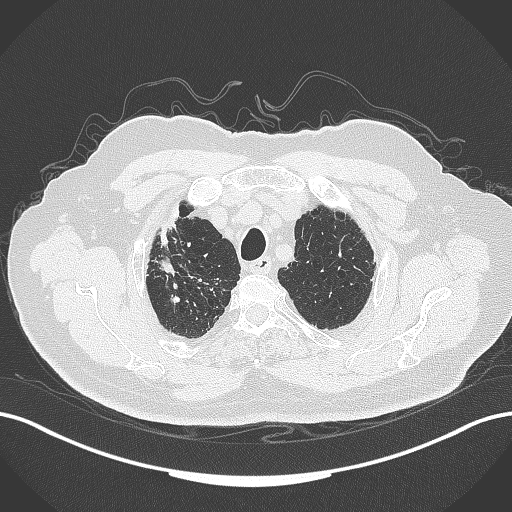
Chest CT, one axial slice; reconstruction kernel B70f; 120 kVp; lung window (W 1500 / L -600 HU); 512 × 512 image matrix, field of view 400 × 400 mm. Male patient, age 72 years. From the clinical record (not read from this slice): clinical TNM (as recorded): T1a N0 M0.
Structures marked on this image (bounding box drawn by a radiologist):
- lung tumour (recorded histology: squamous cell carcinoma): bounding box <162,200,188,275> (left, top, right, bottom; pixels)